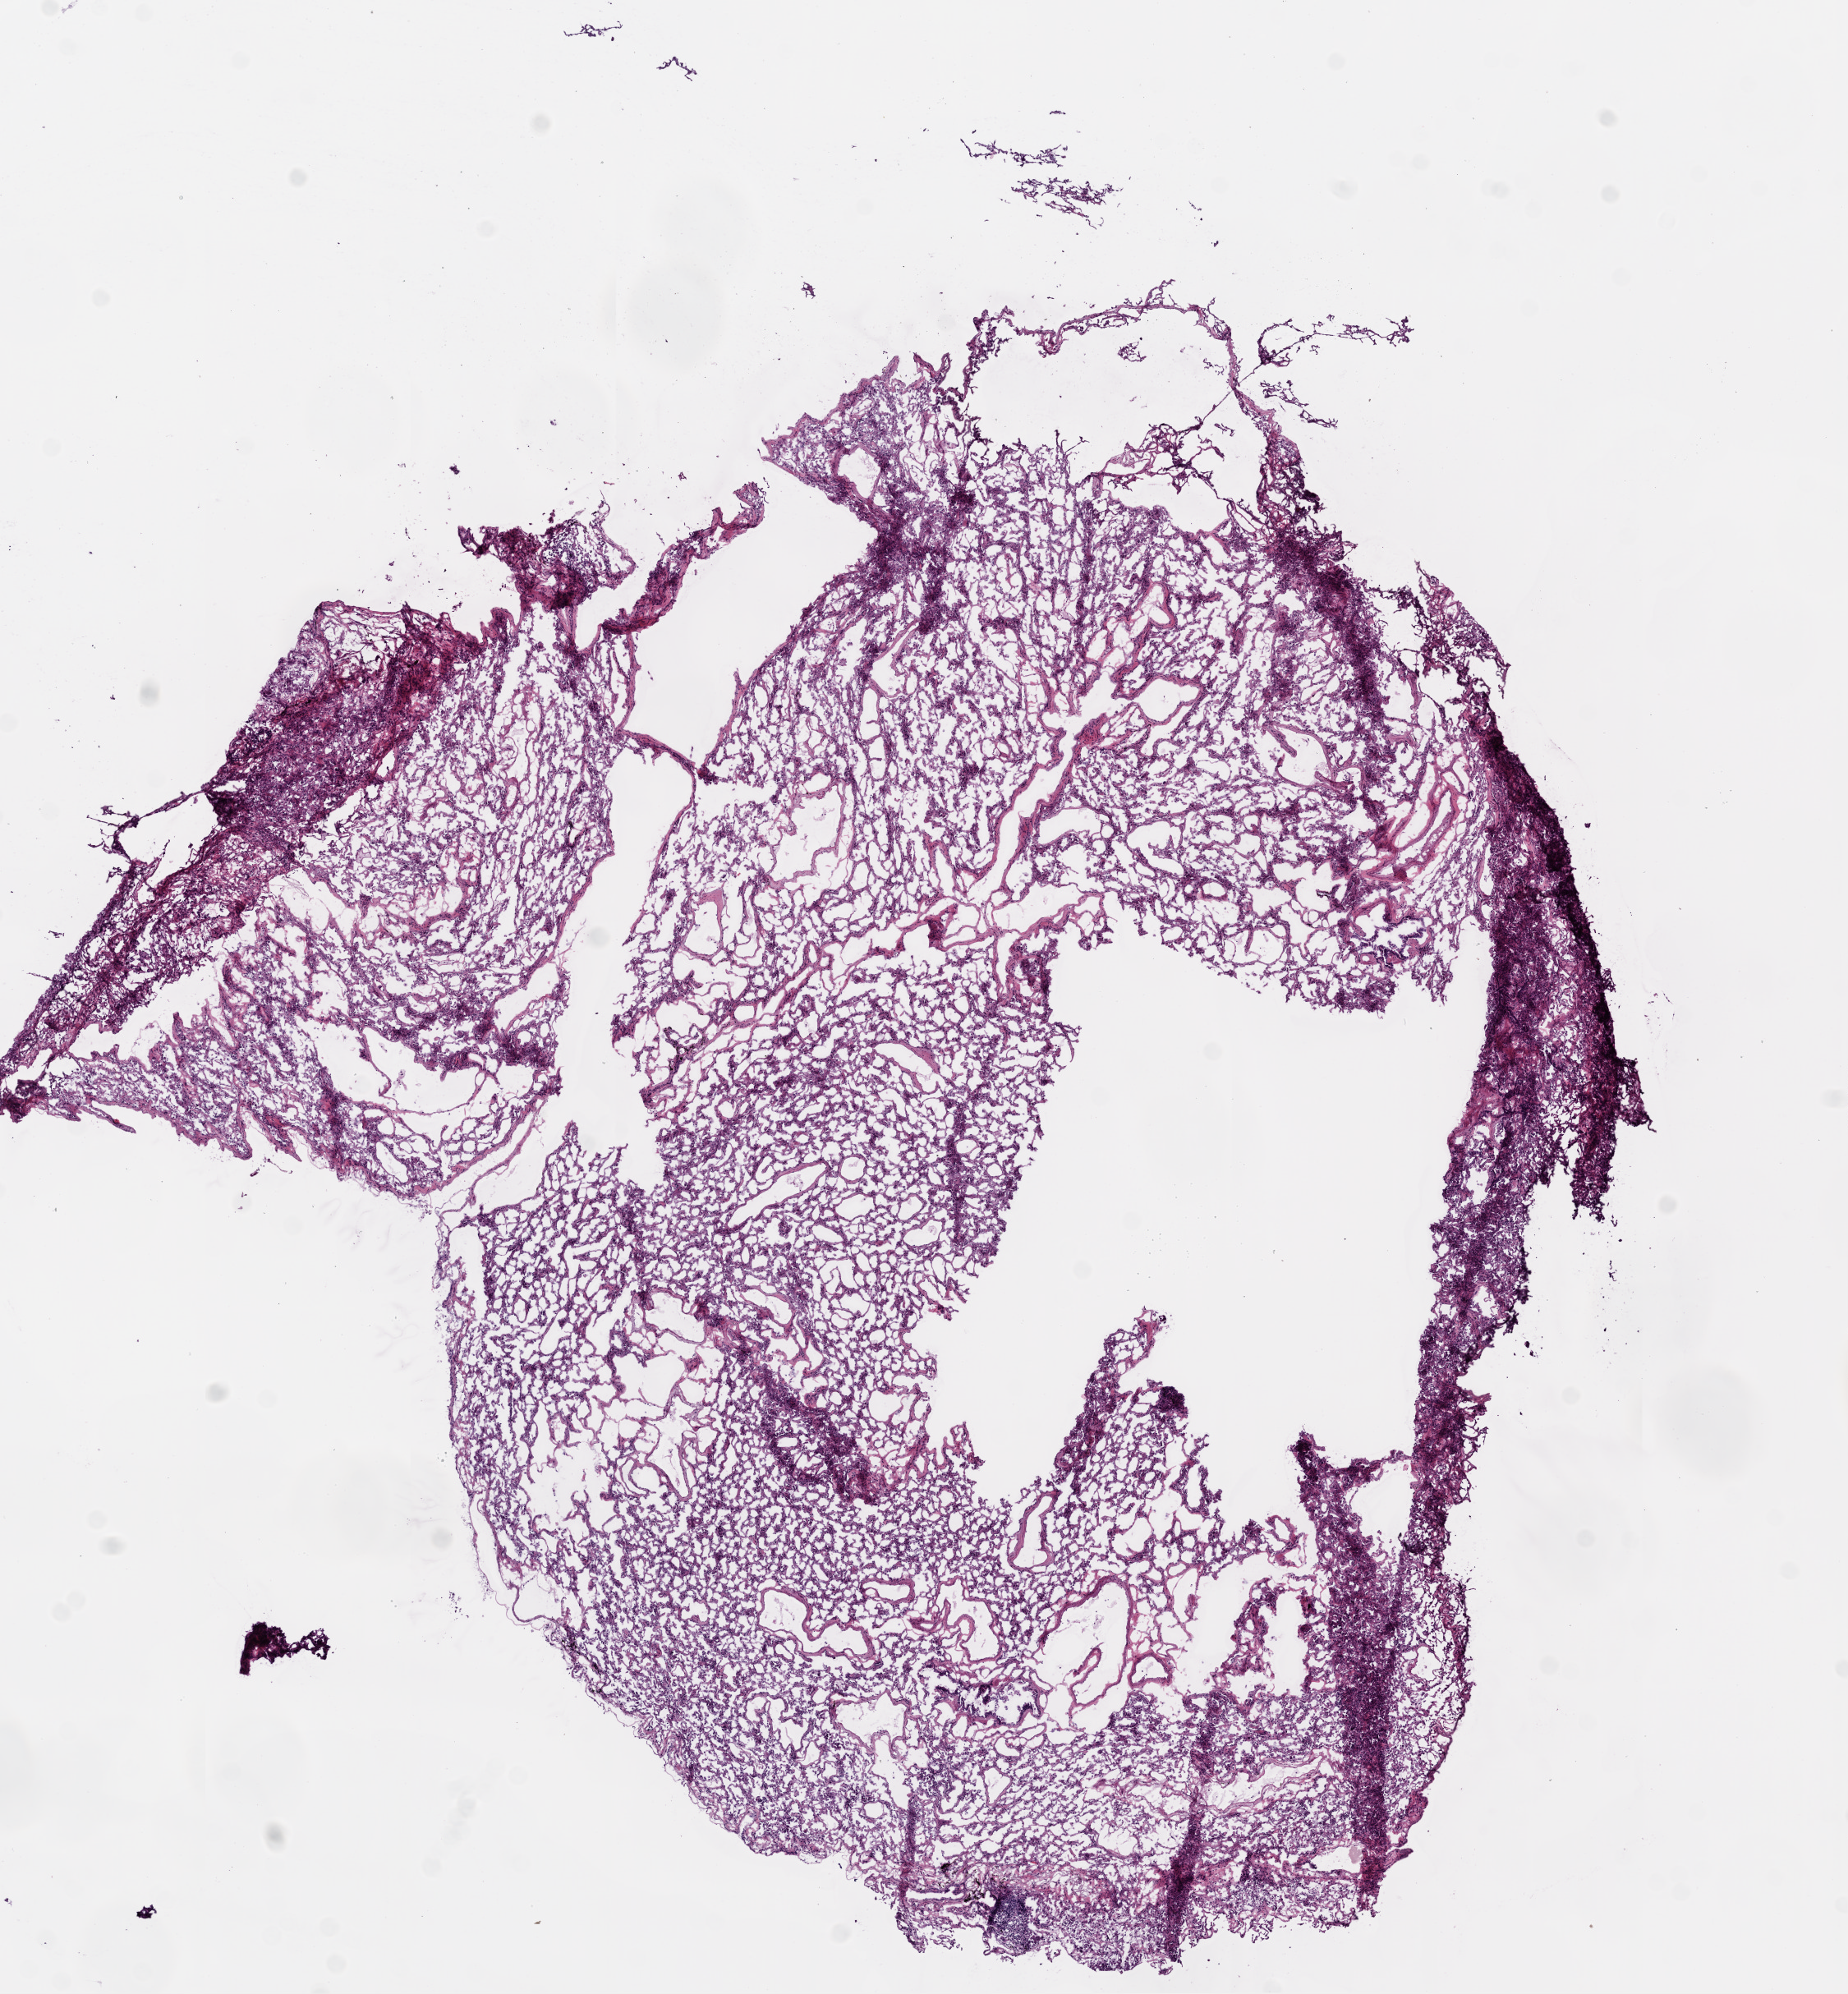
Whole-slide histology image, H&E-stained — low-resolution overview of the scanned area, about 9.0 x 9.7 mm (acquisition: 20x scan). Frozen section from the bottom of the tissue portion. Sample: solid tissue normal (non-tumour tissue), lung. Male patient; age at initial diagnosis 72 years.
This section: solid tissue normal (non-tumour) sample from the same patient. Patient diagnosis: Adenocarcinoma, NOS (lower lobe, lung).